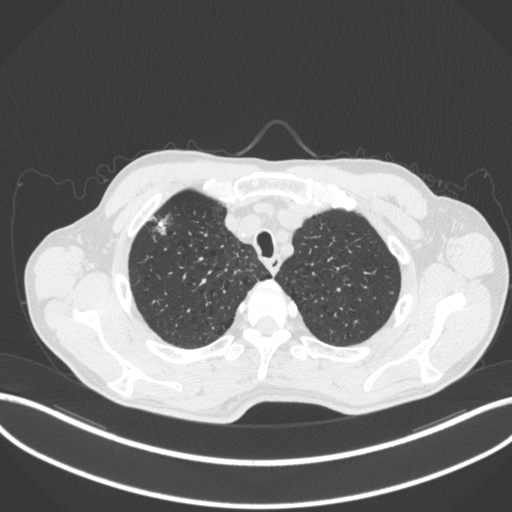
Chest CT, one axial slice; position 360 of 414 along the scan axis; reconstruction kernel B31f; lung window (W 1500 / L -600 HU); 1 mm slice thickness; 512 × 512 image matrix, field of view 400 × 400 mm. Patient: male, 69 years. Case-level facts recorded for this patient, not image findings: clinical TNM (as recorded): T1b N1 M0.
Structures marked on this image (rectangle marked by the reading radiologist):
- lung tumour (recorded histology: adenocarcinoma): bounding box (x1, y1, x2, y2) in pixels: (151, 214, 175, 240)